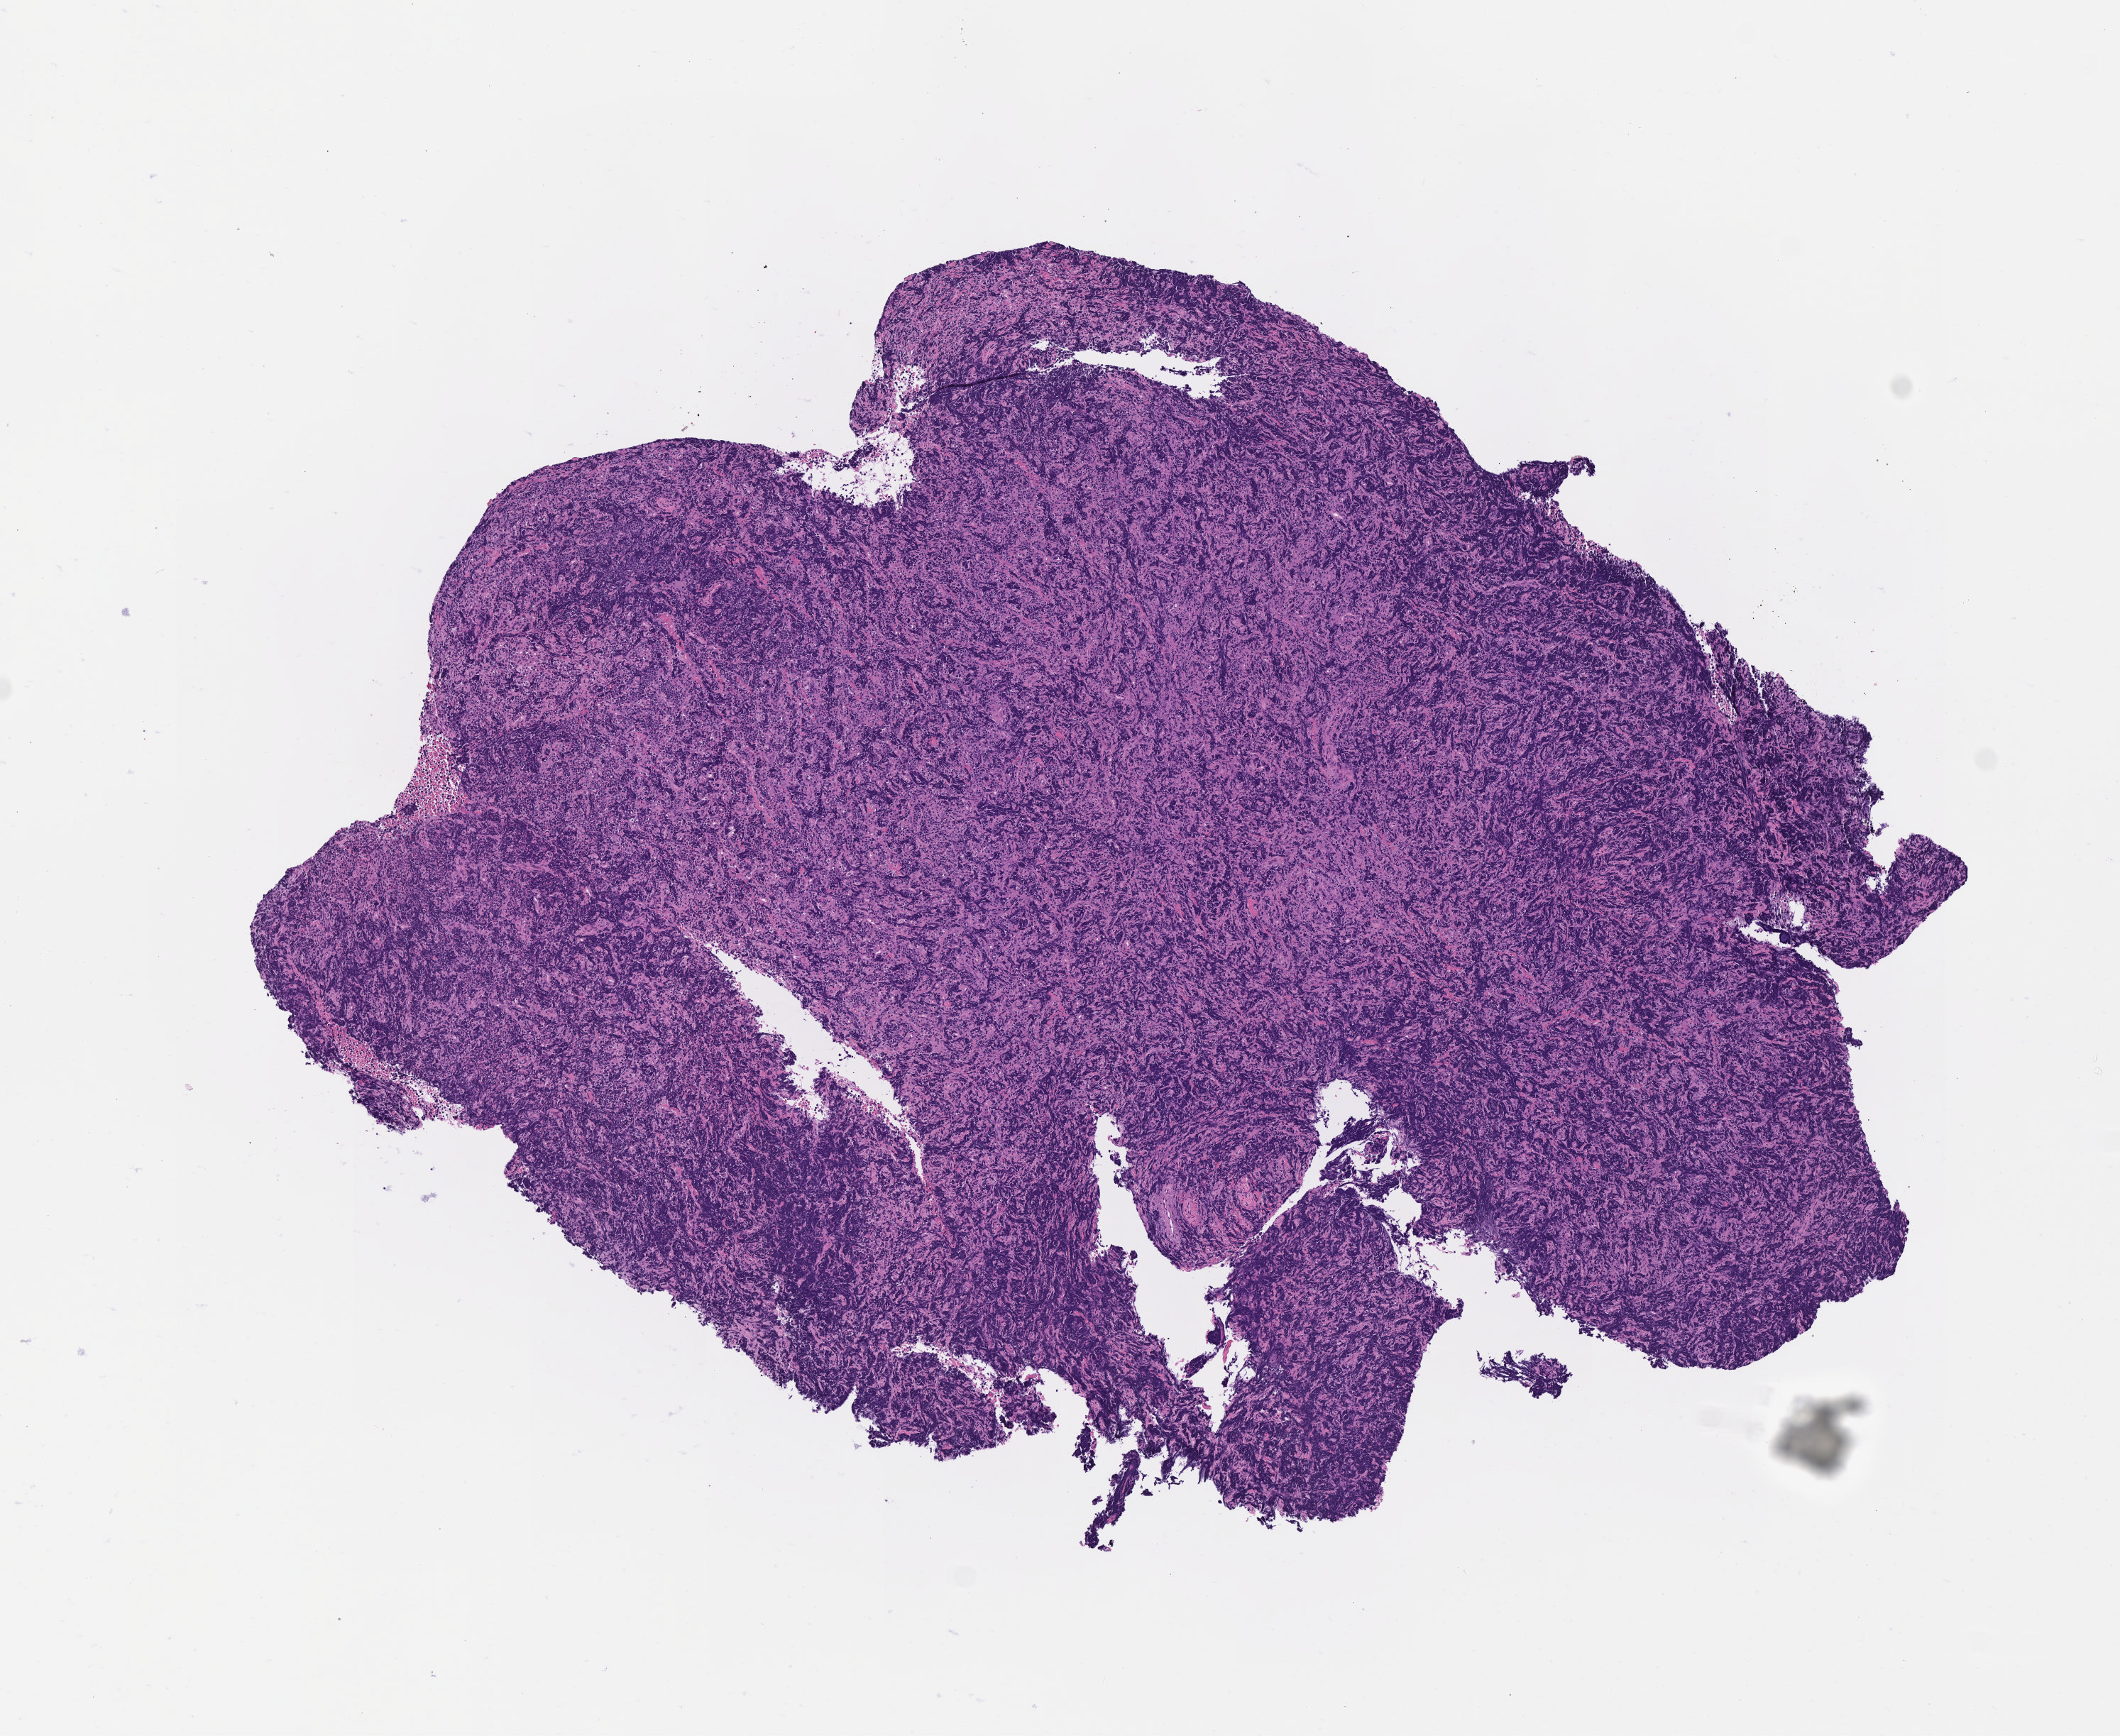
Digitized H&E-stained section — whole scanned area (about 6.0 x 4.9 mm) shown as a low-resolution overview; tumor tissue; site: mandible. Male patient; age at initial diagnosis 8 years.
Histologic diagnosis: Burkitt lymphoma, NOS.